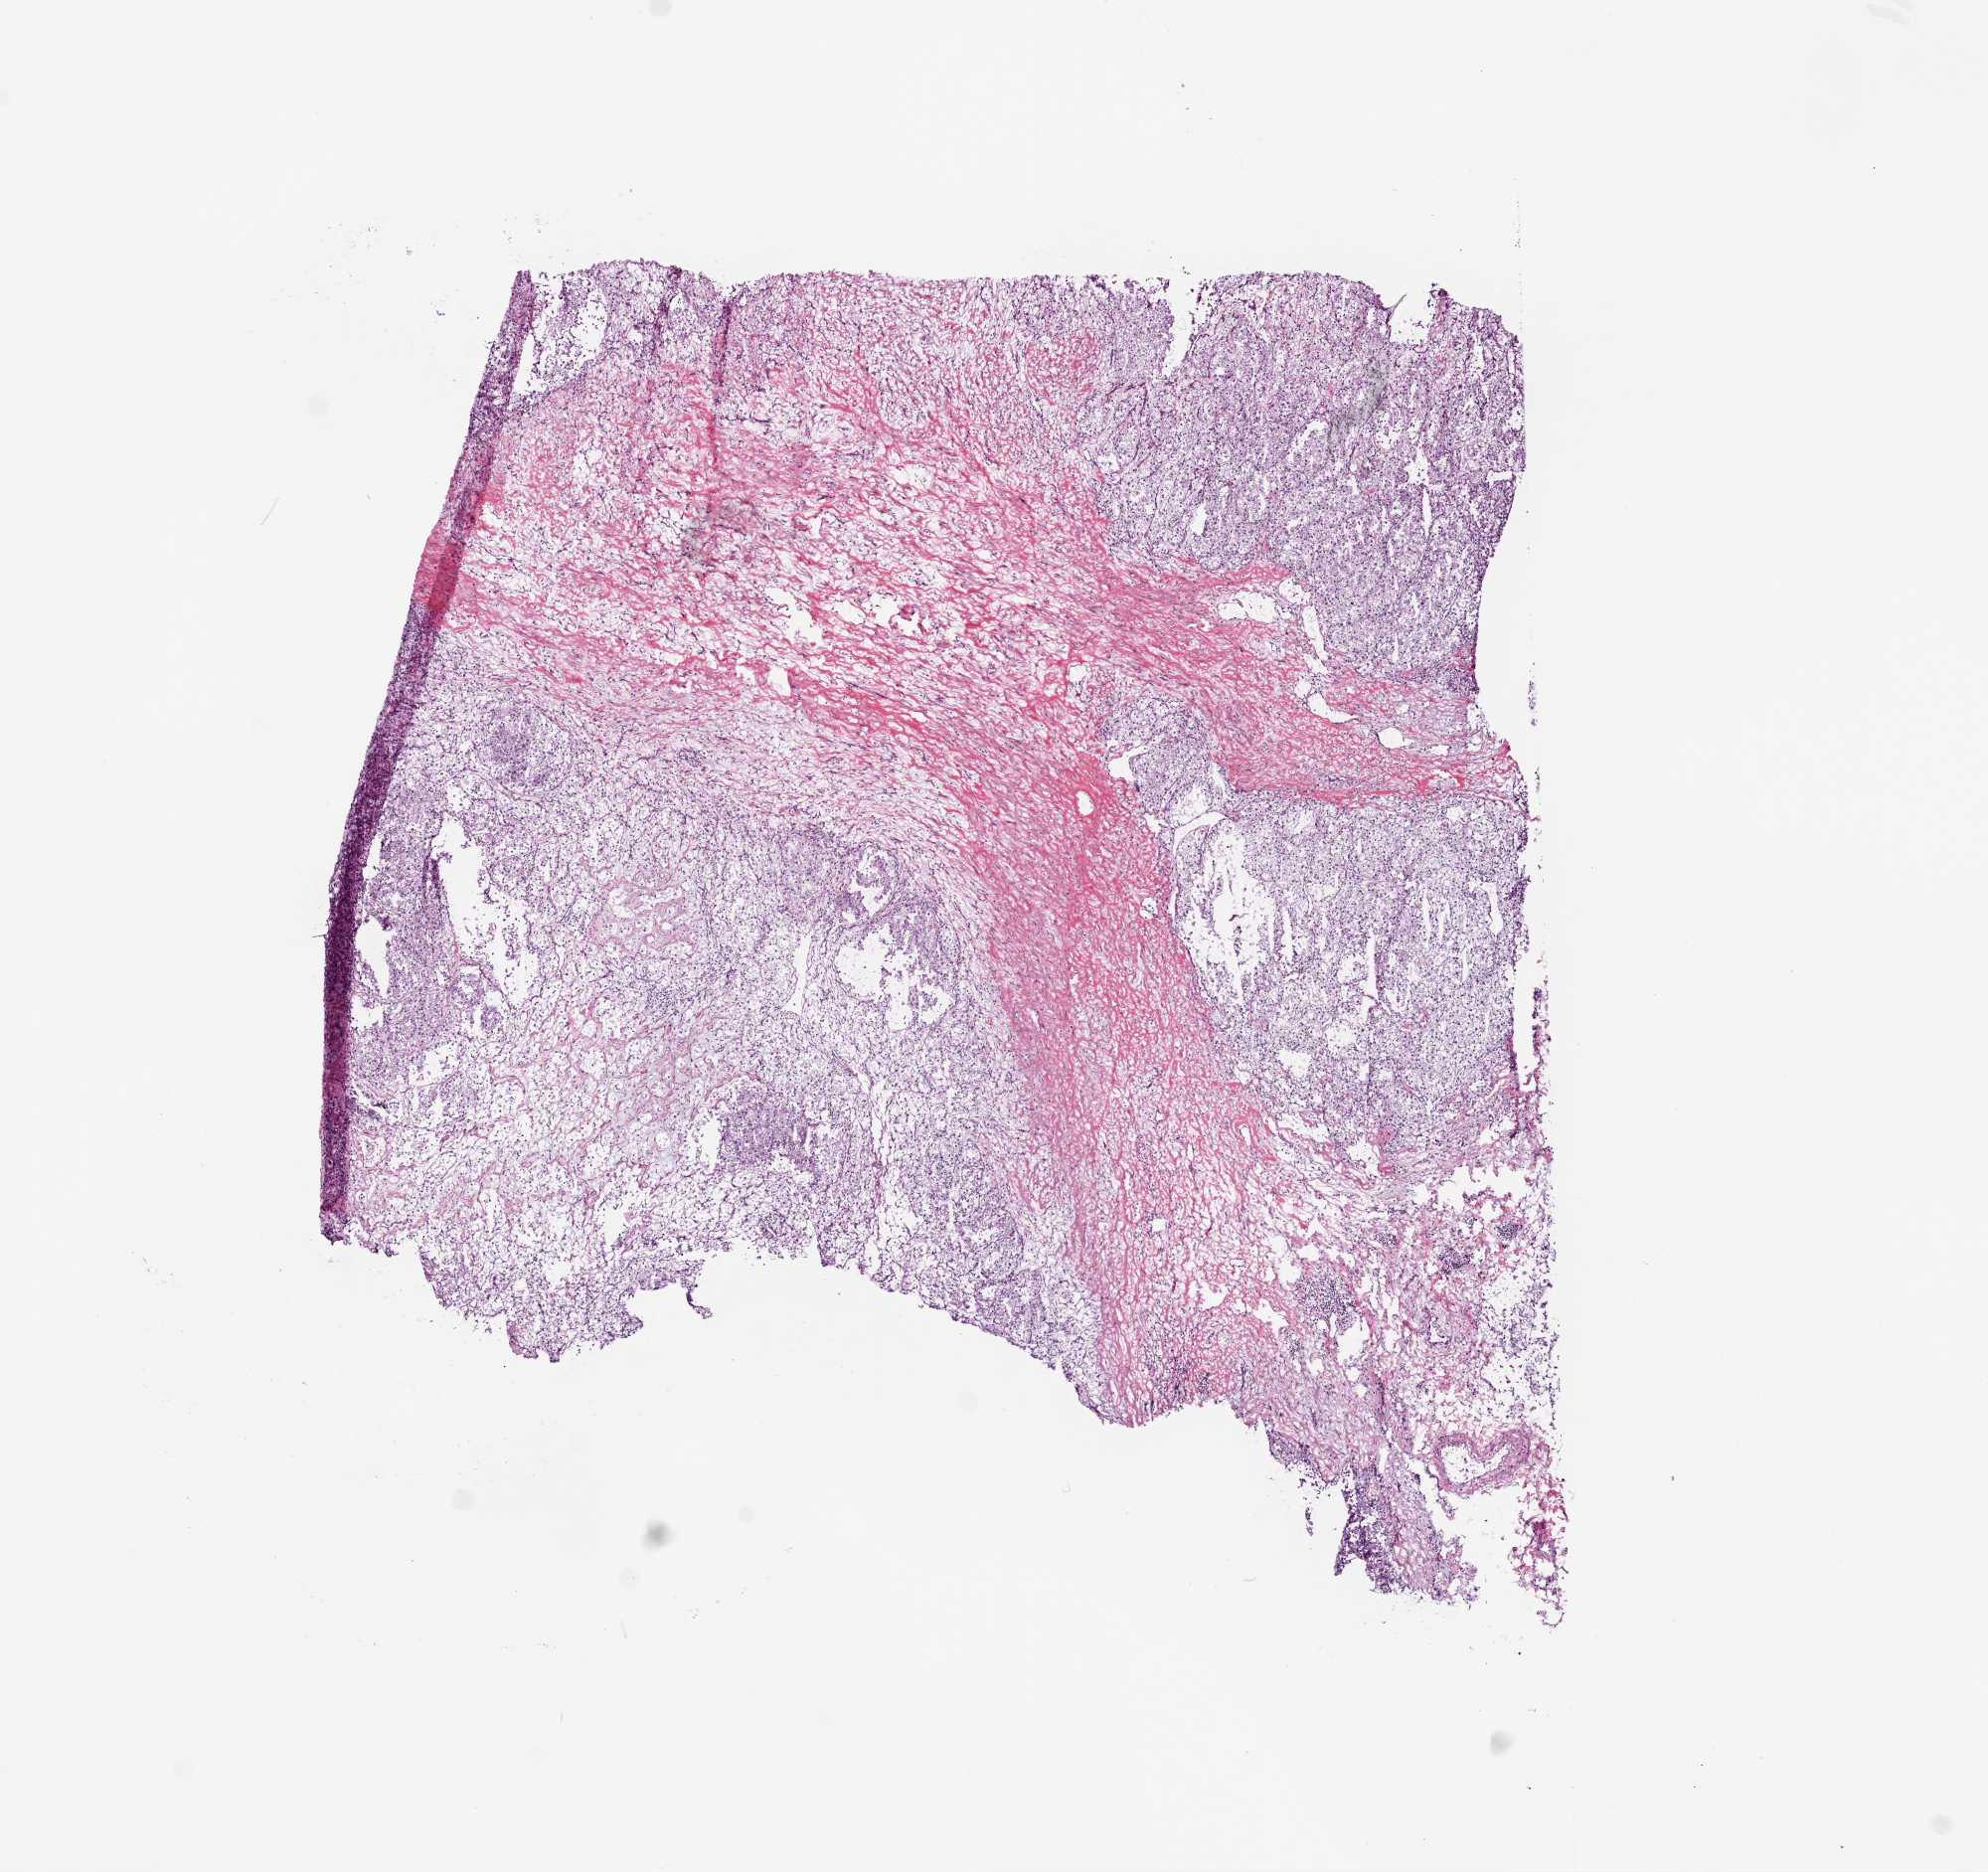
Hematoxylin and eosin (H&E) stained whole-slide image, a low-resolution overview of the entire scanned area, about 8.0 x 7.6 mm (from a 20x scan), frozen section, primary tumour sample from the kidney. Male, age 71 years at initial diagnosis. Histologic grade: G3 (poorly differentiated). Pathologist review of this section (percent, as recorded): tumour cells 75%, tumour nuclei 85%, normal cells 0%, stromal cells 25%, necrosis 0%.
- diagnosis: Clear cell adenocarcinoma, NOS
- lymph nodes positive (case pathology): 0 of 3 examined
- AJCC pathologic stage: III (7th edition)
- laterality: right